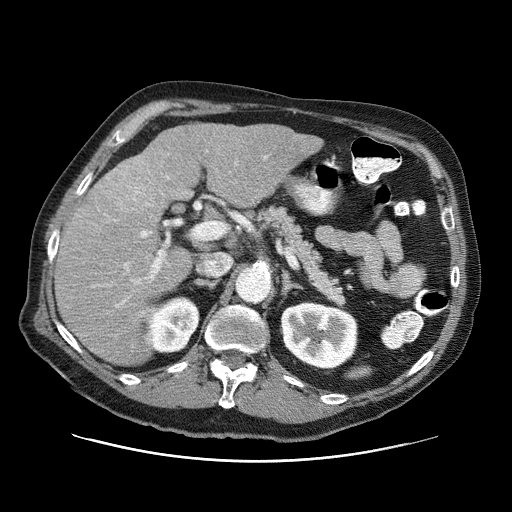
Contrast-enhanced abdominal CT (liver protocol), one axial slice; position 39 of 87 along the scan axis; reconstruction kernel STANDARD; 120 kVp; one of 3 acquisitions stored at this slice position; soft-tissue window (W 400 / L 40 HU); 2.5 mm slice thickness; 512 × 512 image matrix, field of view 400 × 400 mm. Case-level facts recorded for this patient, not image findings: diagnosis: hepatocellular carcinoma (patient treated with transarterial chemoembolisation; whether this scan precedes or follows treatment is not stated here); TNM stage (as recorded): Stage-IIIA; Child-Pugh class: A; tumour size: 6 cm.
Structures marked on this image (semi-automatically segmented with operator editing):
- liver parenchyma outside the tumour (the mass and vessels are separate outlines, so this box may not span the whole liver): box from (x=54, y=124) to (x=322, y=364) px
- mass: (x=93, y=149)–(x=169, y=218)
- liver vessels: (x=93, y=156)–(x=268, y=313)